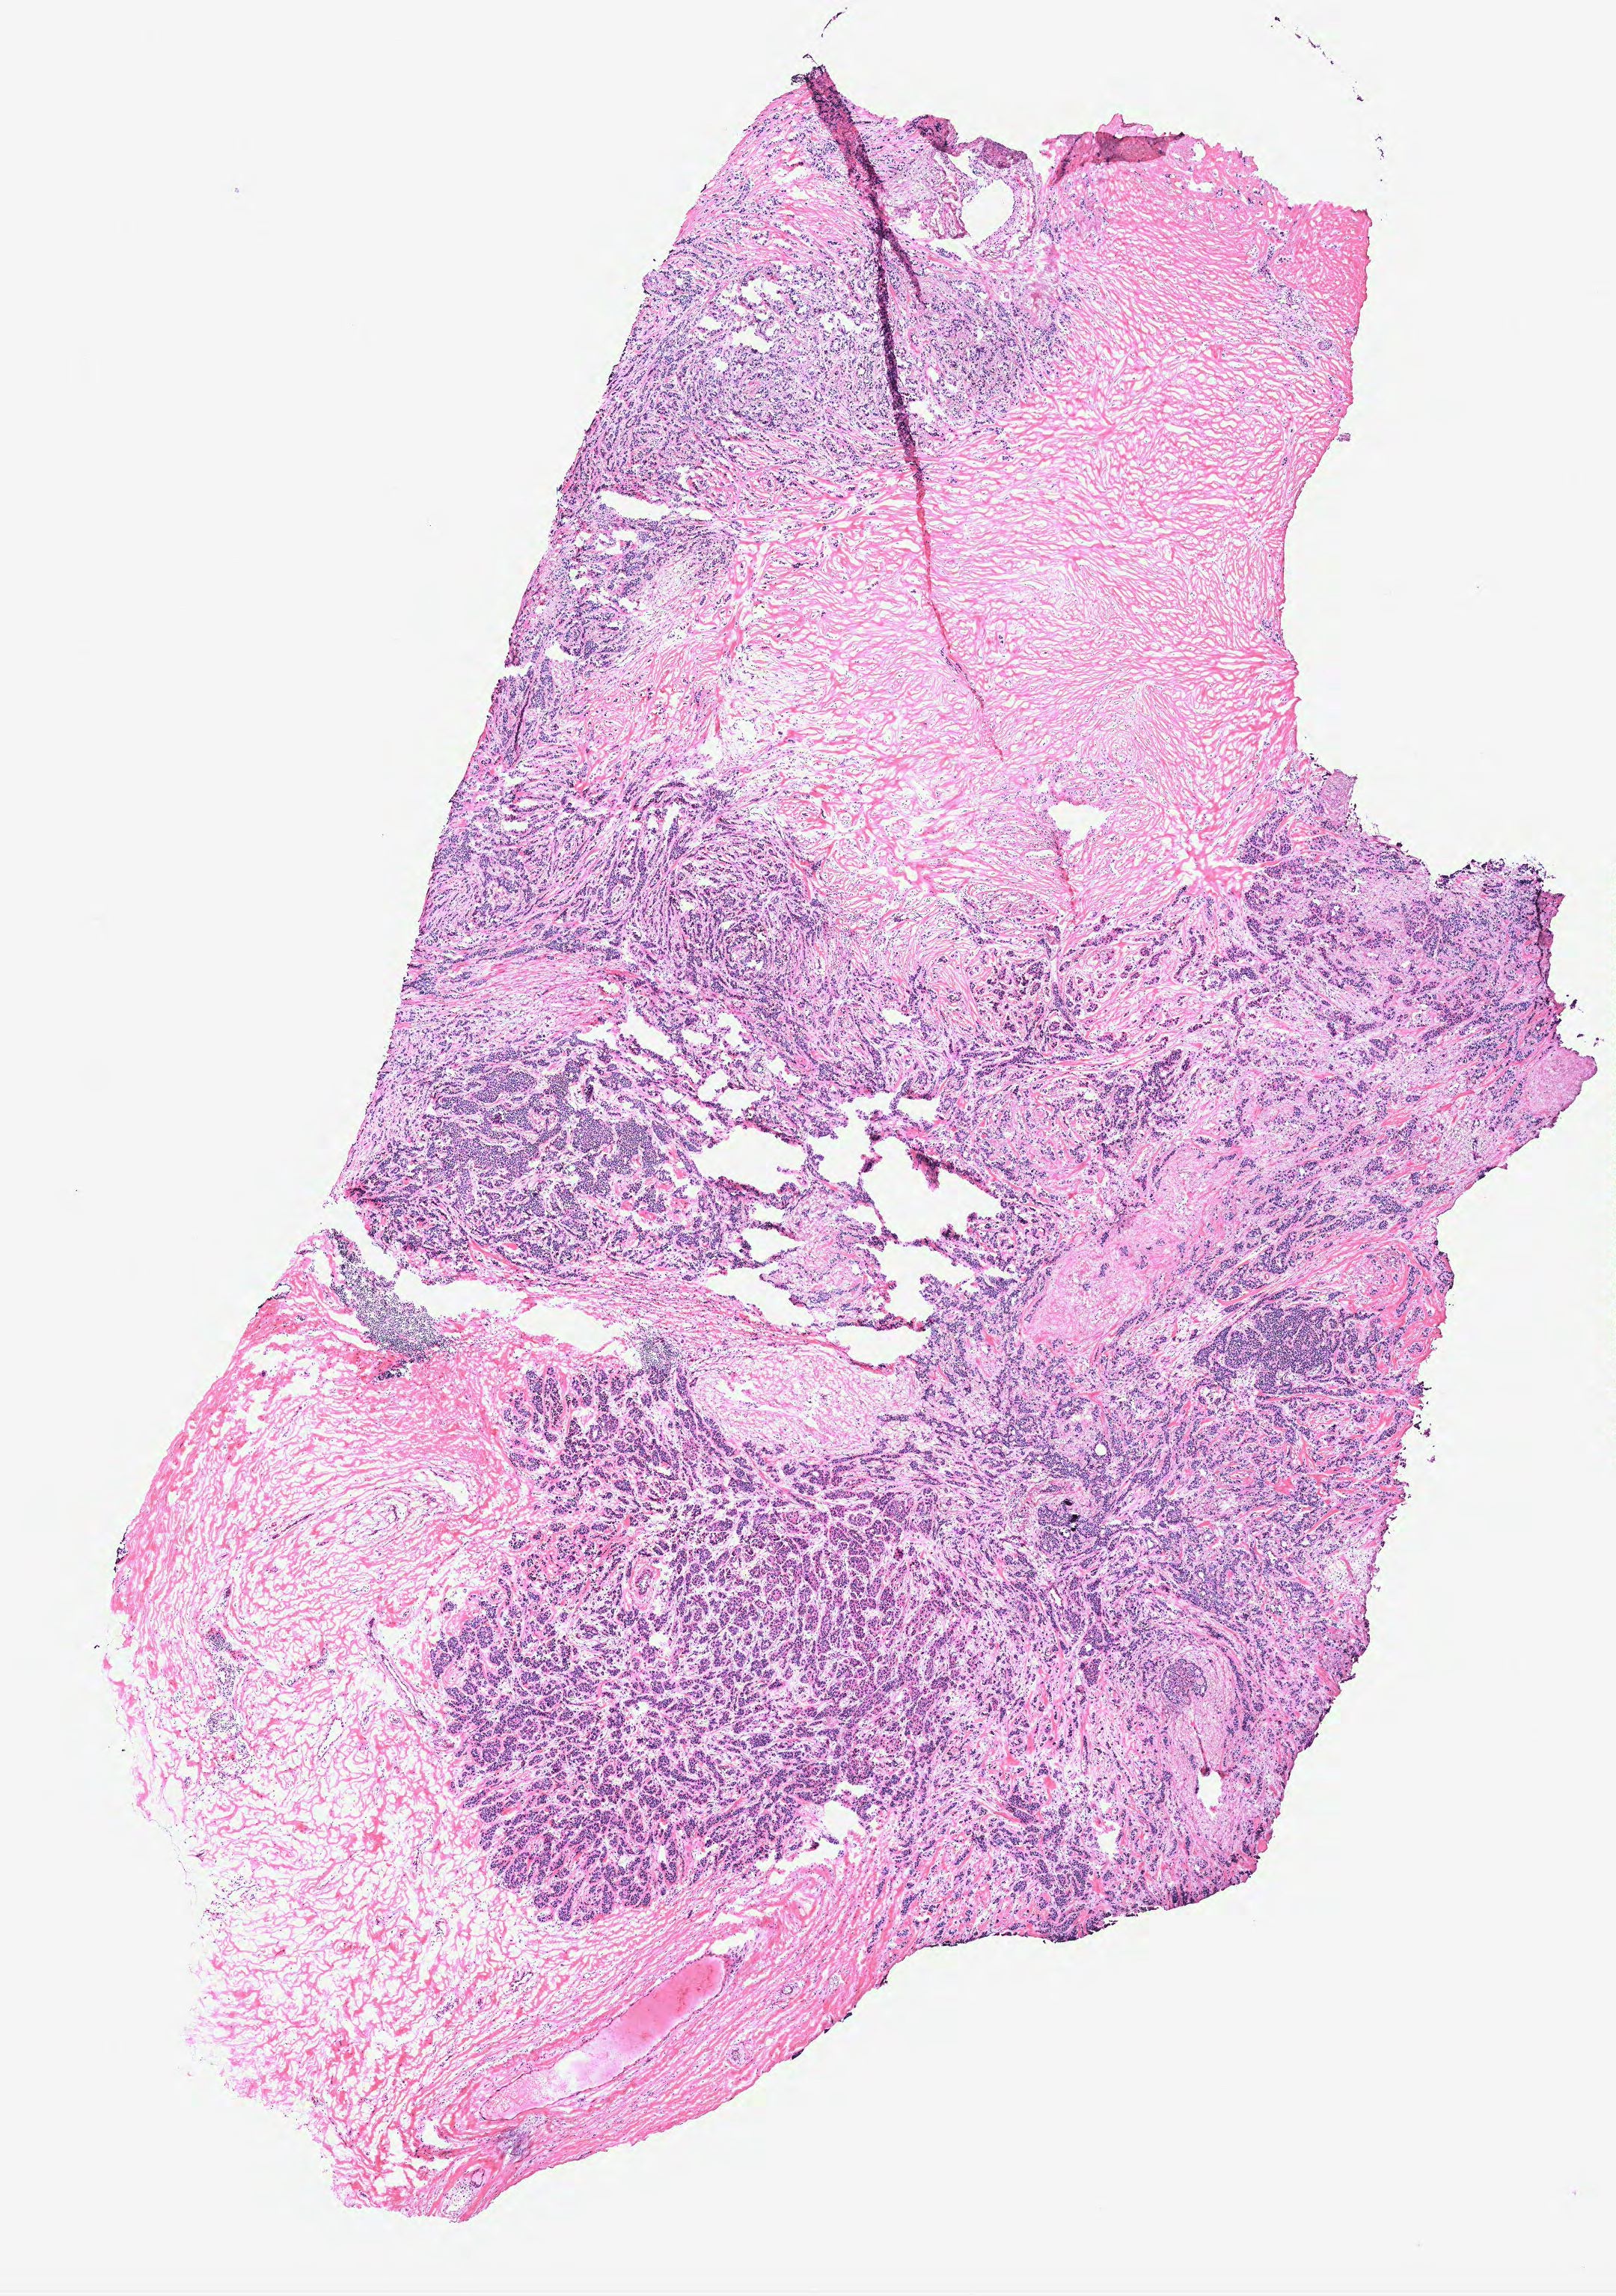
Hematoxylin and eosin (H&E) stained whole-slide image — low-resolution overview of the scanned area, about 8.6 x 12.3 mm. Breast, tissue type not recorded.
* patient diagnosis (cohort enrolment): breast cancer (breast)